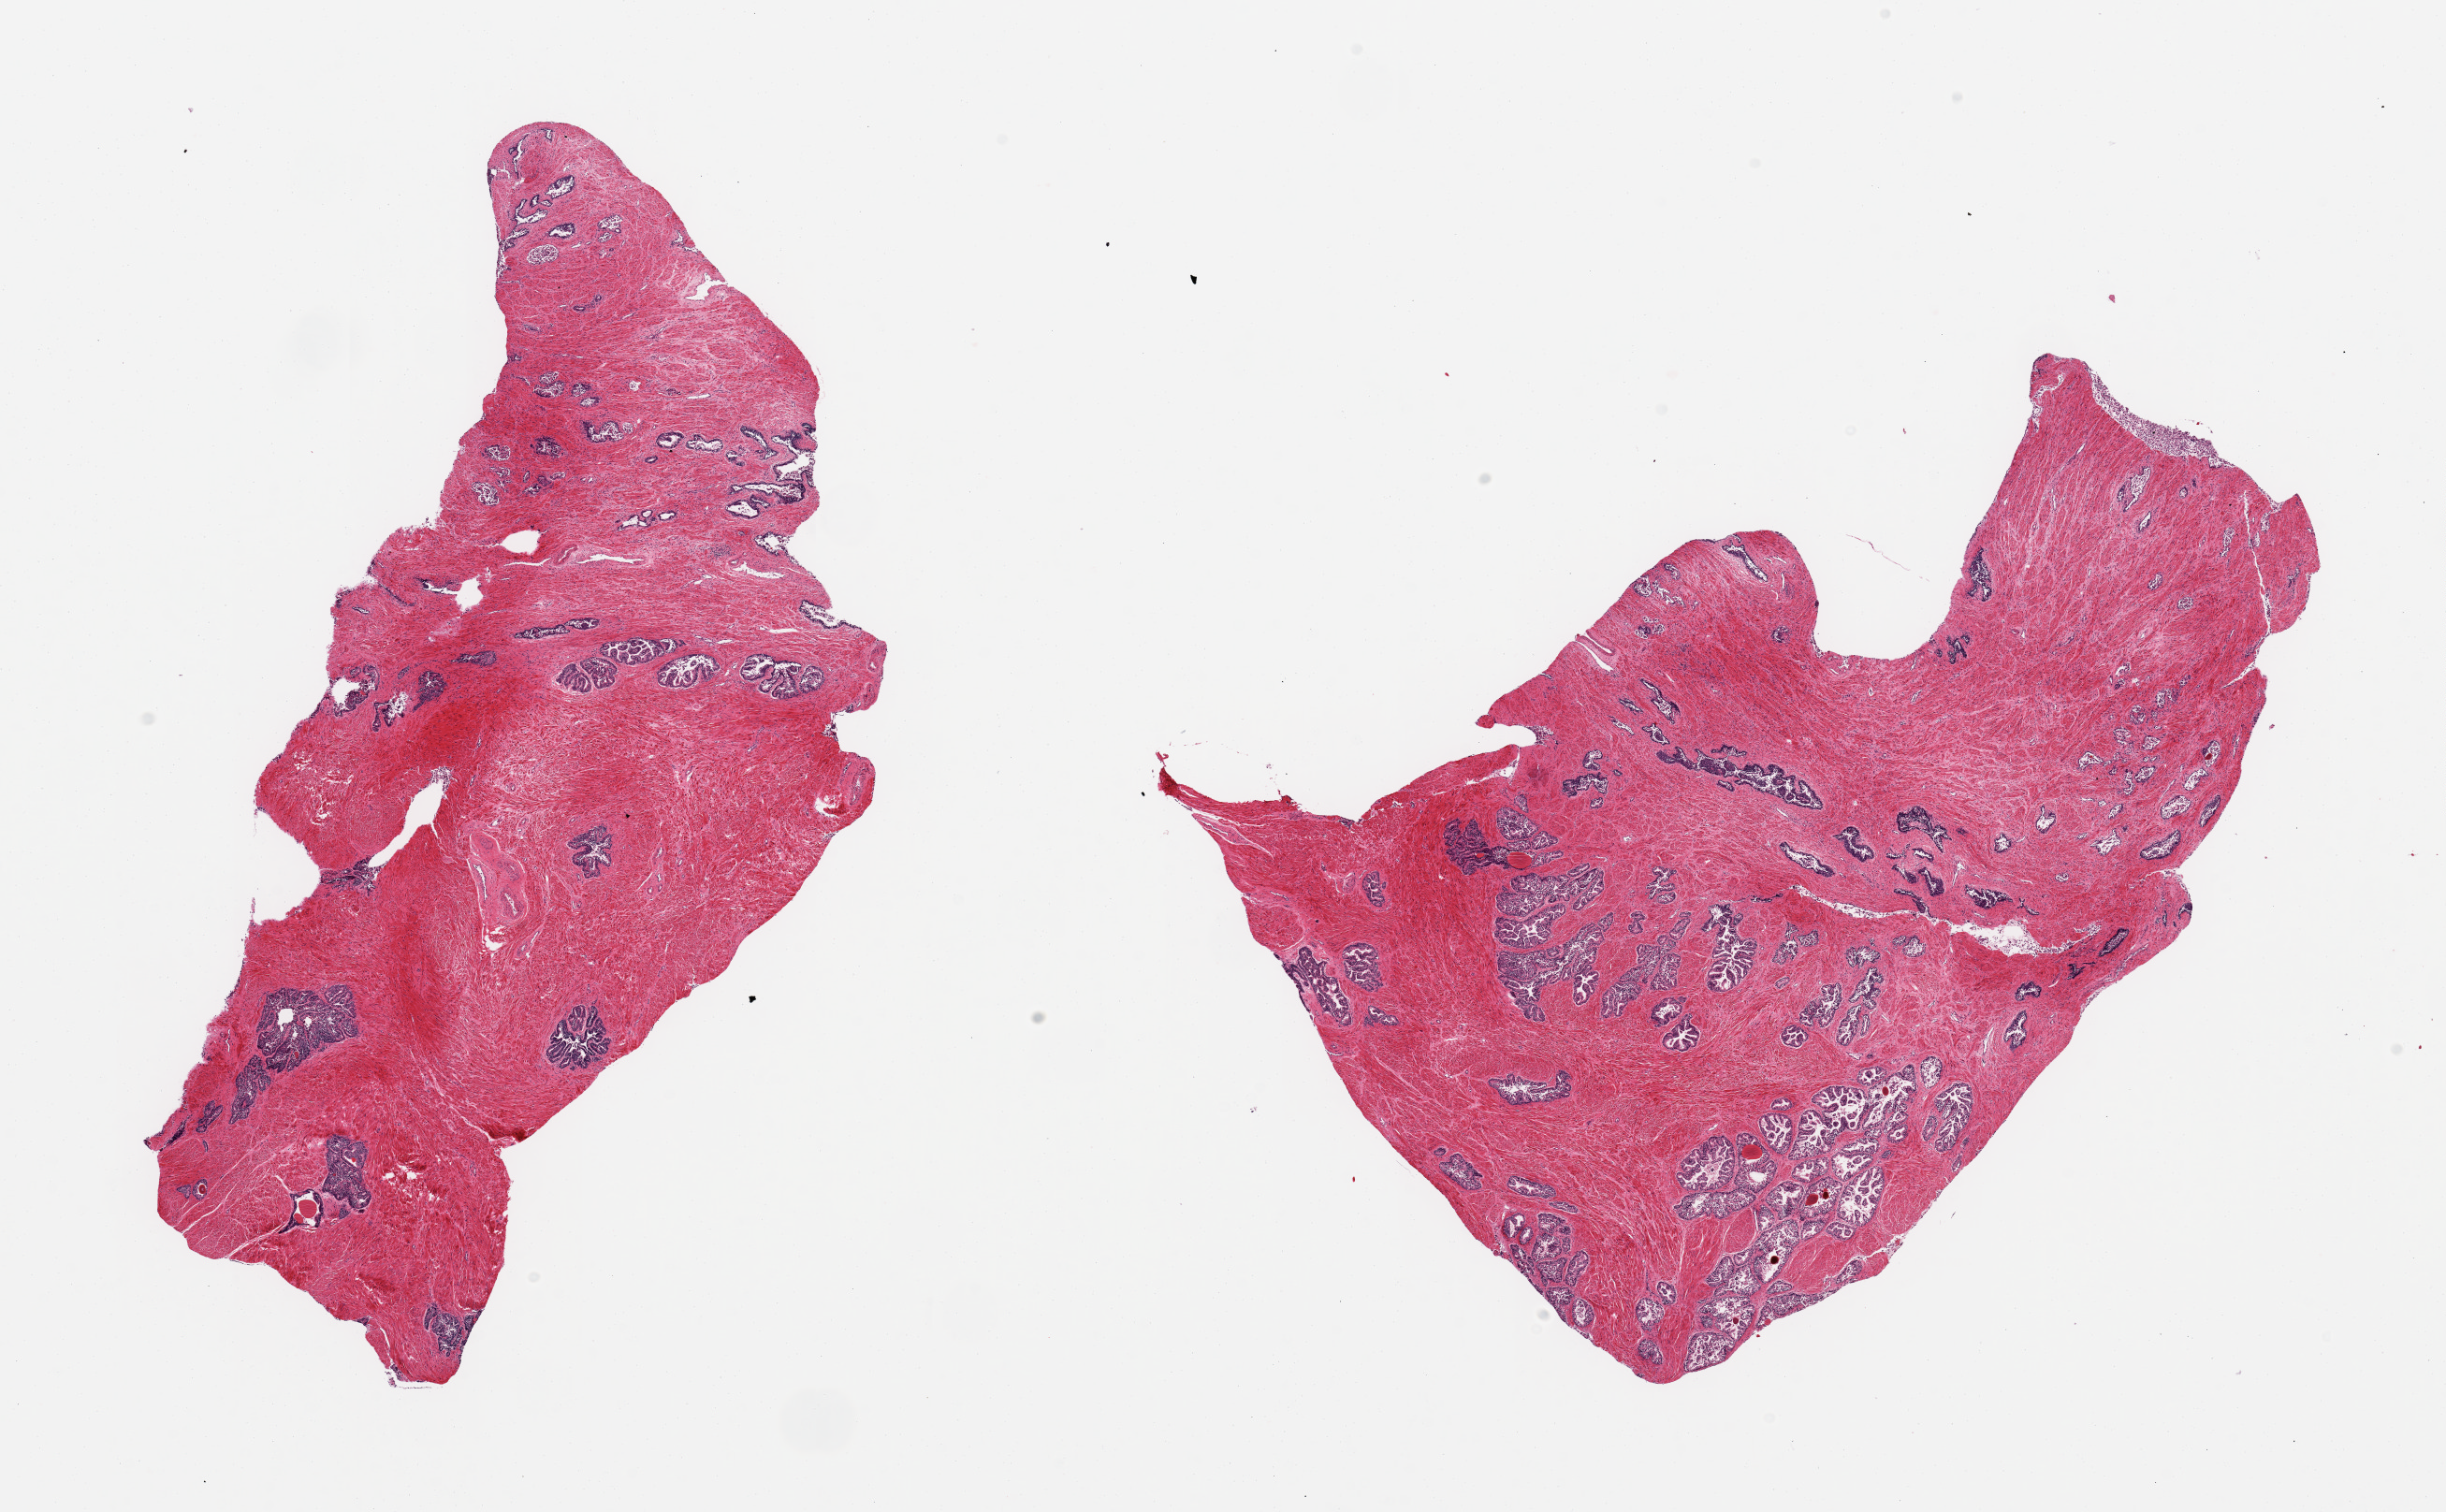
Whole-slide image, hematoxylin and eosin (H&E) stain, brightfield, low-resolution overview of the scanned area, about 20.7 x 12.8 mm (slide scanned at 20x); PAXgene-fixed paraffin-embedded (PFPE) section; section of prostate (target tissue); tissue donor sample. Male donor.
Pathologist's review note for this sample: 2 pieces; no hyperplasia.